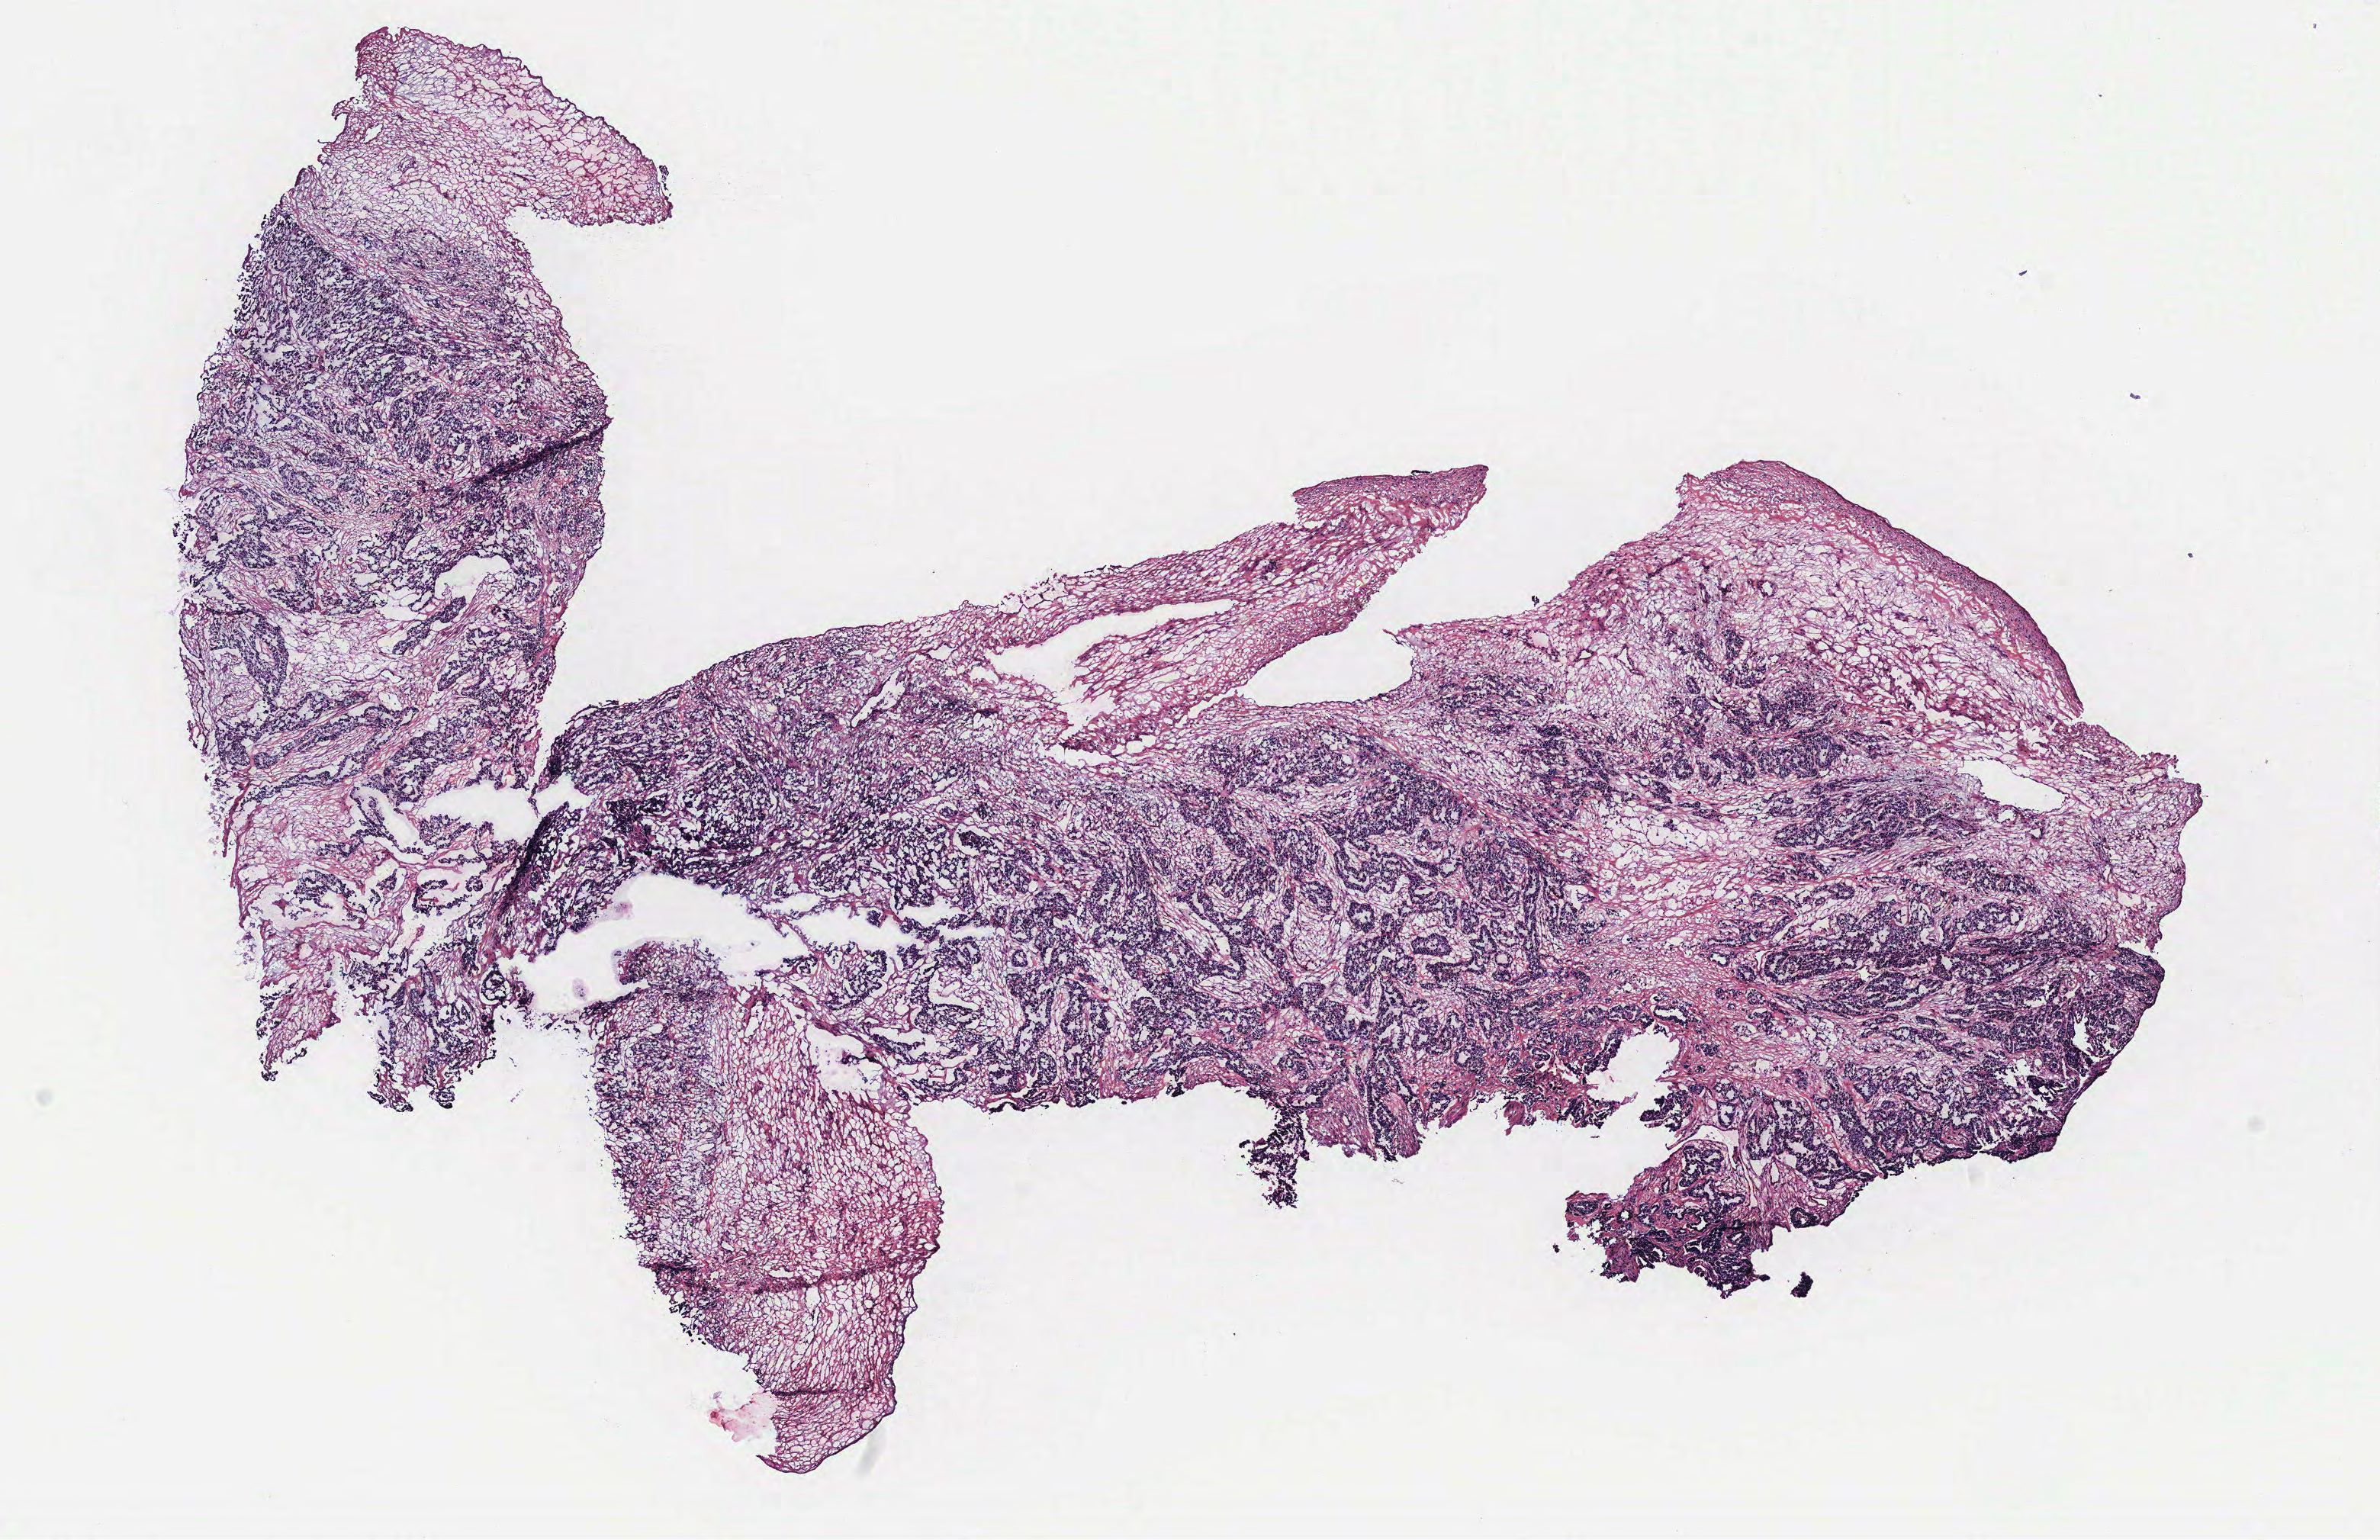
H&E whole-slide image, shown as a low-resolution overview of the whole scanned area (about 12.5 x 8.1 mm, acquisition: 40x scan). Ovary, normal (non-tumour) tissue. 58-year-old female patient.
* this section: normal (non-tumour) tissue from the same patient
* patient diagnosis: Serous adenocarcinoma, NOS (peritoneum, NOS)